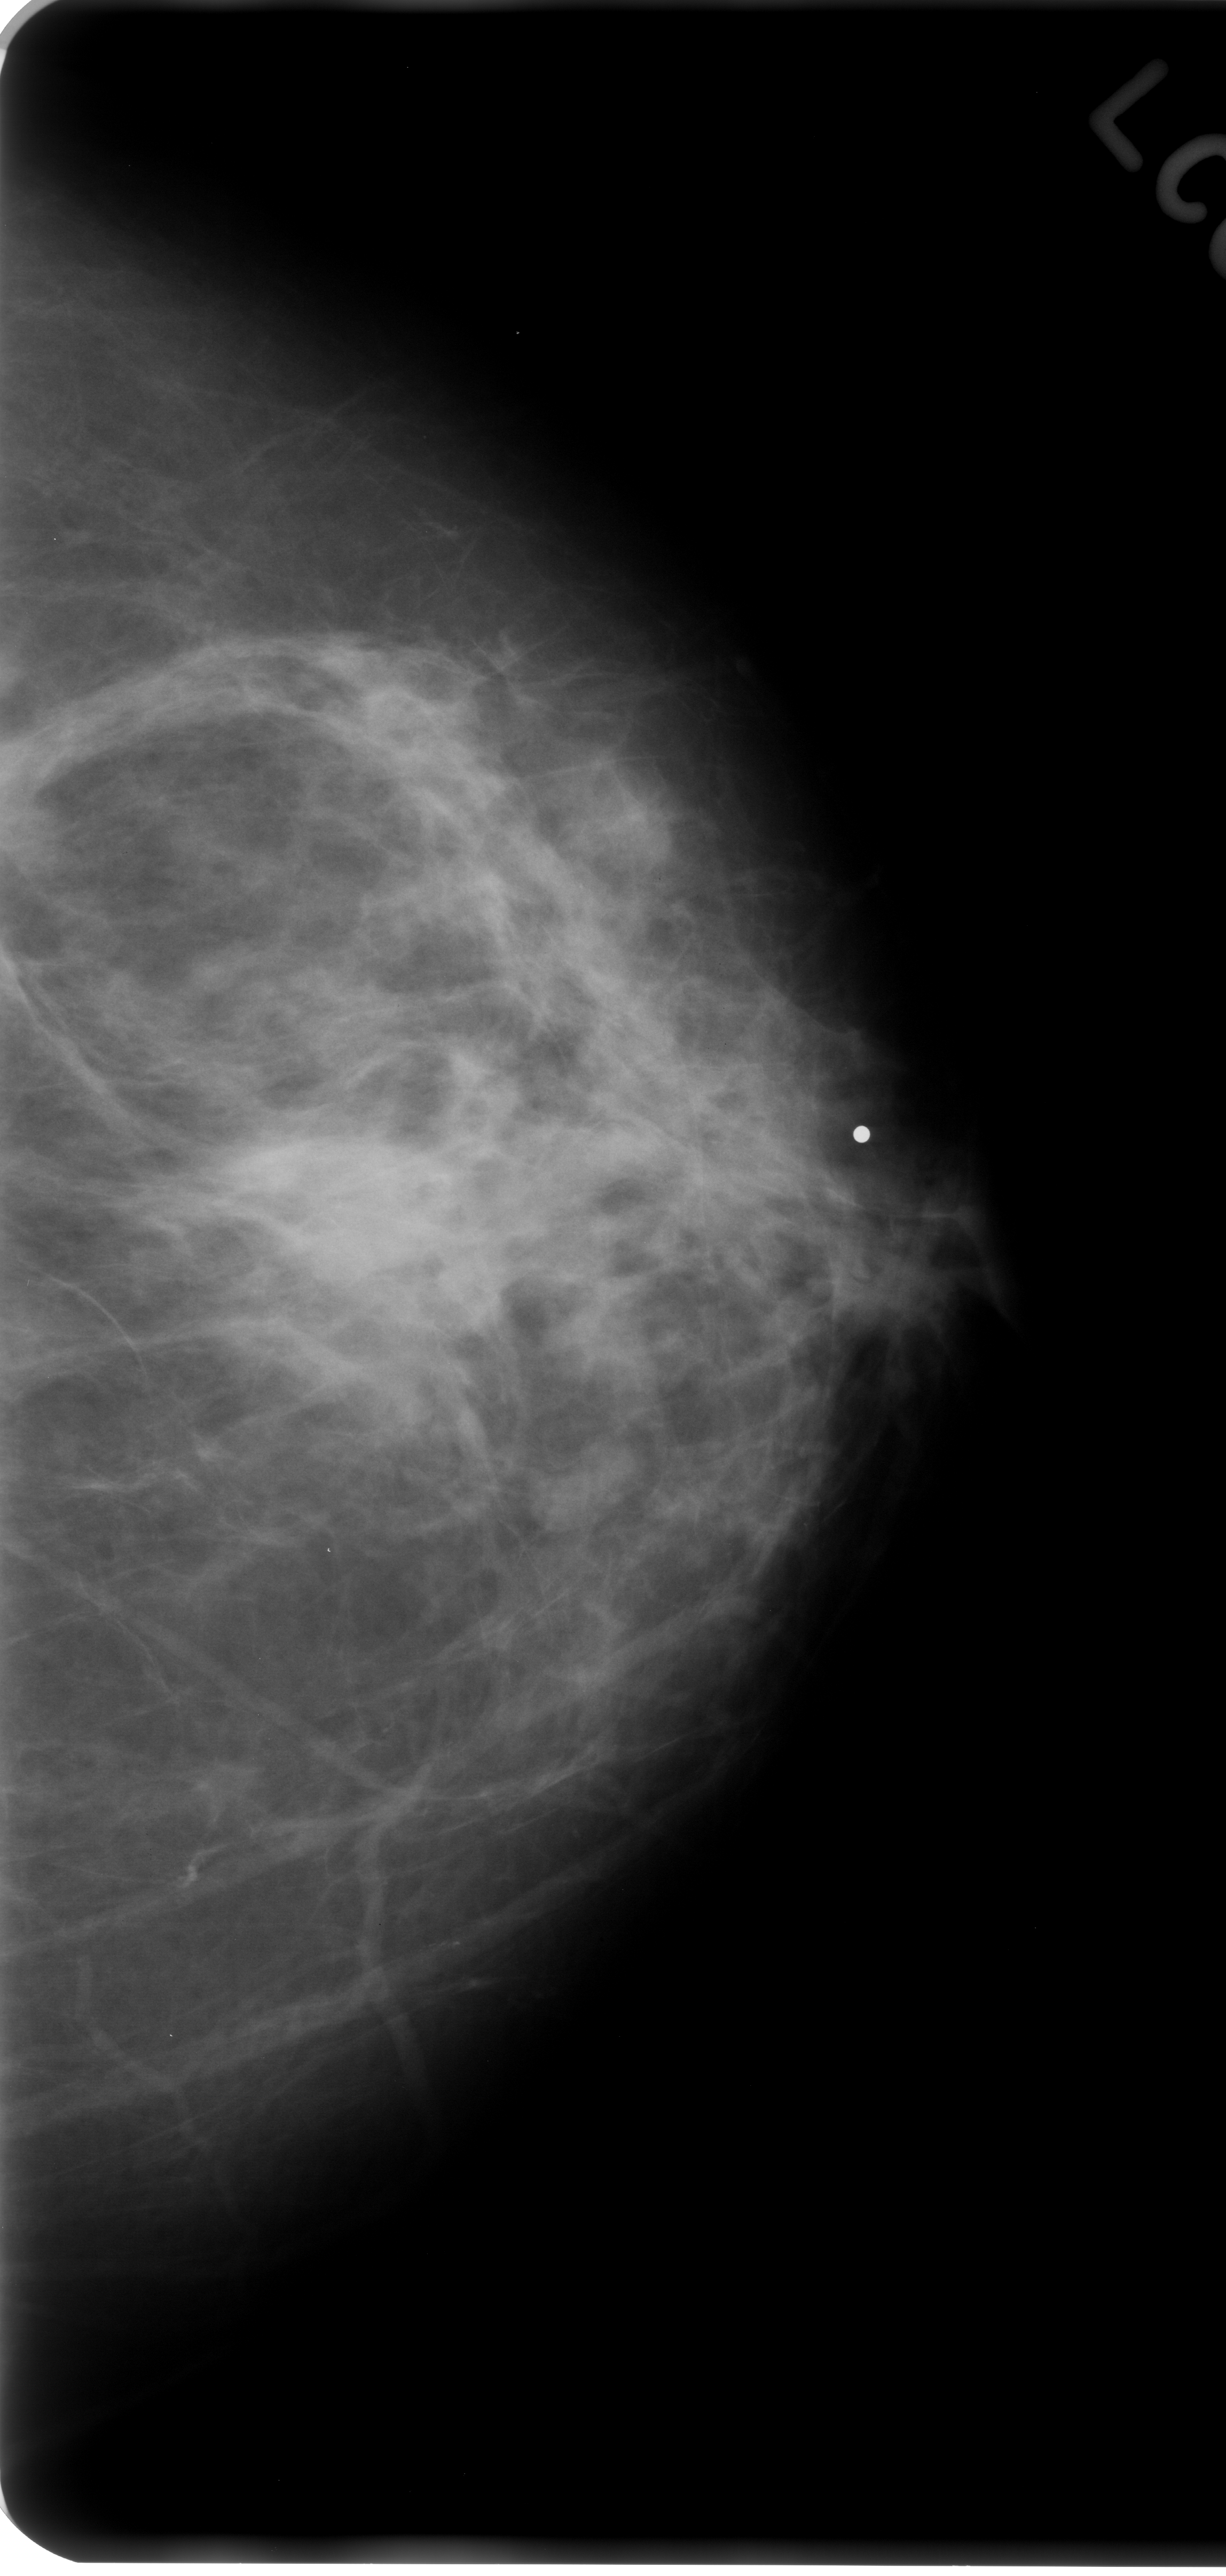
Digitized screen-film mammogram. Left breast. CC view. BI-RADS breast density category 2 (scale 1–4). 1226 × 2576 image matrix.
Expert-marked regions of interest on this image (one box per marked abnormality):
- mass, shape irregular, margins ill defined; BI-RADS assessment category 4; subtlety rating 4 on a 1 (subtle) to 5 (obvious) scale; pathology result (as recorded, not read from the image): malignant: bounding box [x1, y1, x2, y2] px = [234, 1111, 524, 1403]